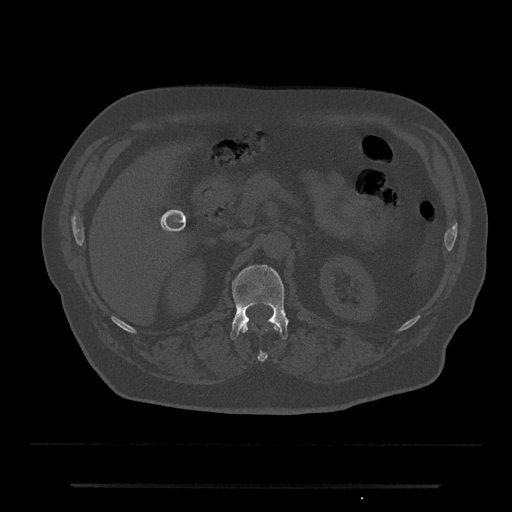
CT including the spine, one axial slice; position 552 of 797 along the scan axis; reconstruction kernel Br40s/3; bone window (W 1800 / L 400 HU); 0.5 mm slice thickness; 512 × 512 image matrix, field of view 434 × 434 mm. Male patient, age 80 years. Case-level facts recorded for this patient, not image findings: primary cancer: prostate; vertebrae with lytic lesions (as recorded): L1, T11.
Outlined on this slice (semi-automatic segmentation, software-assisted and operator-edited):
- L1 vertebra: box from (x=230, y=265) to (x=302, y=339) px
- T12 vertebra: (x=241, y=325)–(x=280, y=361)